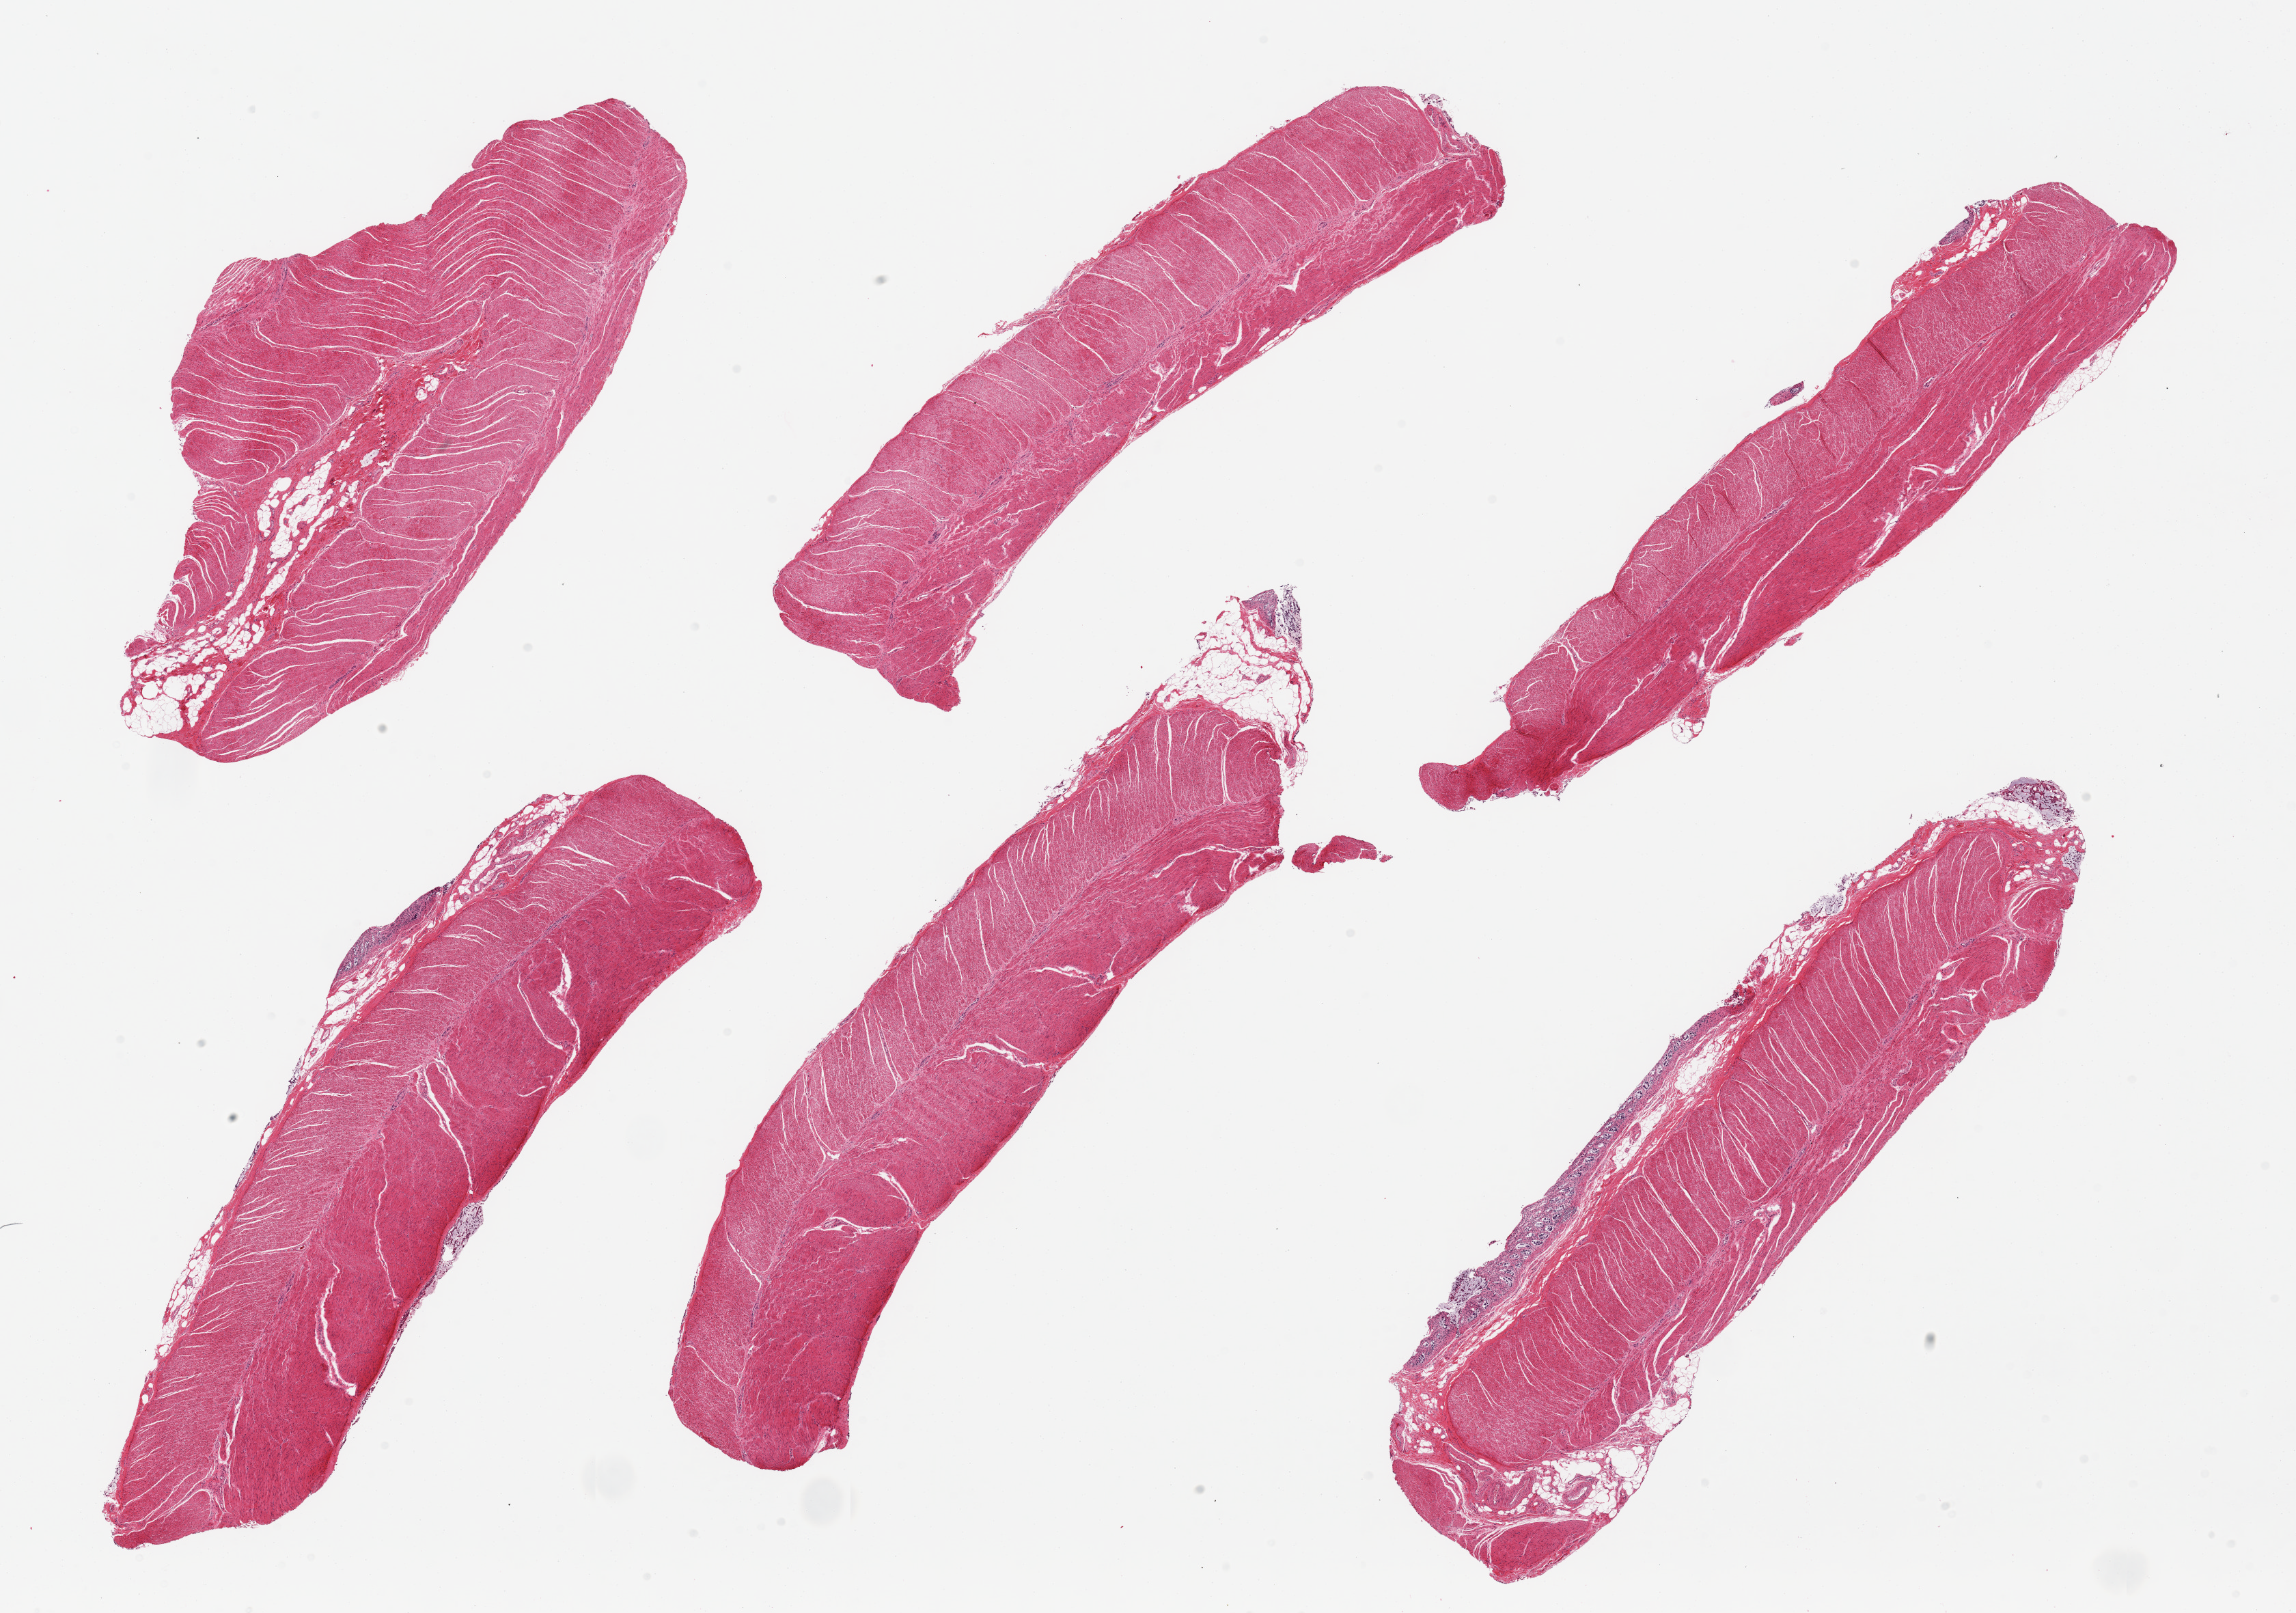
Haematoxylin and eosin whole-slide image — whole scanned area (about 26.6 x 18.7 mm, slide scanned at 20x) shown as a low-resolution overview, PAXgene-fixed paraffin-embedded (PFPE) section, target tissue: sigmoid colon, tissue donor sample. Donor: male.
• review note (as recorded): 6 pieces, target muscularis, trace 'contaminant' autolyzed mucosa